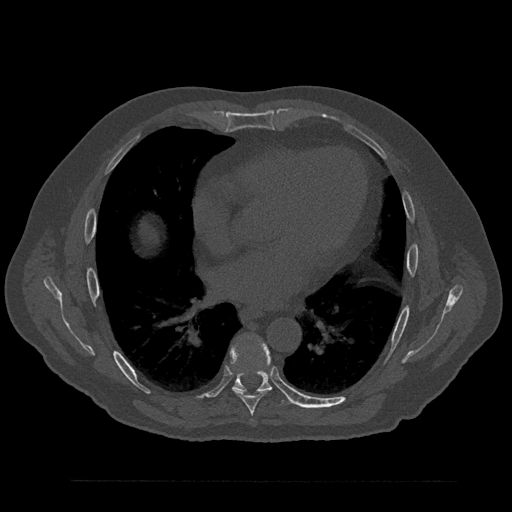
CT including the spine, one axial slice; slice 484 of 797 in the series (ordered by position); reconstruction kernel Br40s/3; 120 kVp; bone window (W 1800 / L 400 HU); 0.5 mm slice thickness; 512 × 512 image matrix, field of view 430 × 430 mm. Male patient, age 61 years. Case-level facts recorded for this patient, not image findings: primary cancer: prostate.
Outlined on this slice (semi-automatic segmentation, software-assisted and operator-edited):
- T7 vertebra: bounding box (x1, y1, x2, y2) in pixels: (230, 344, 265, 421)
- T8 vertebra: (233, 337, 292, 404)